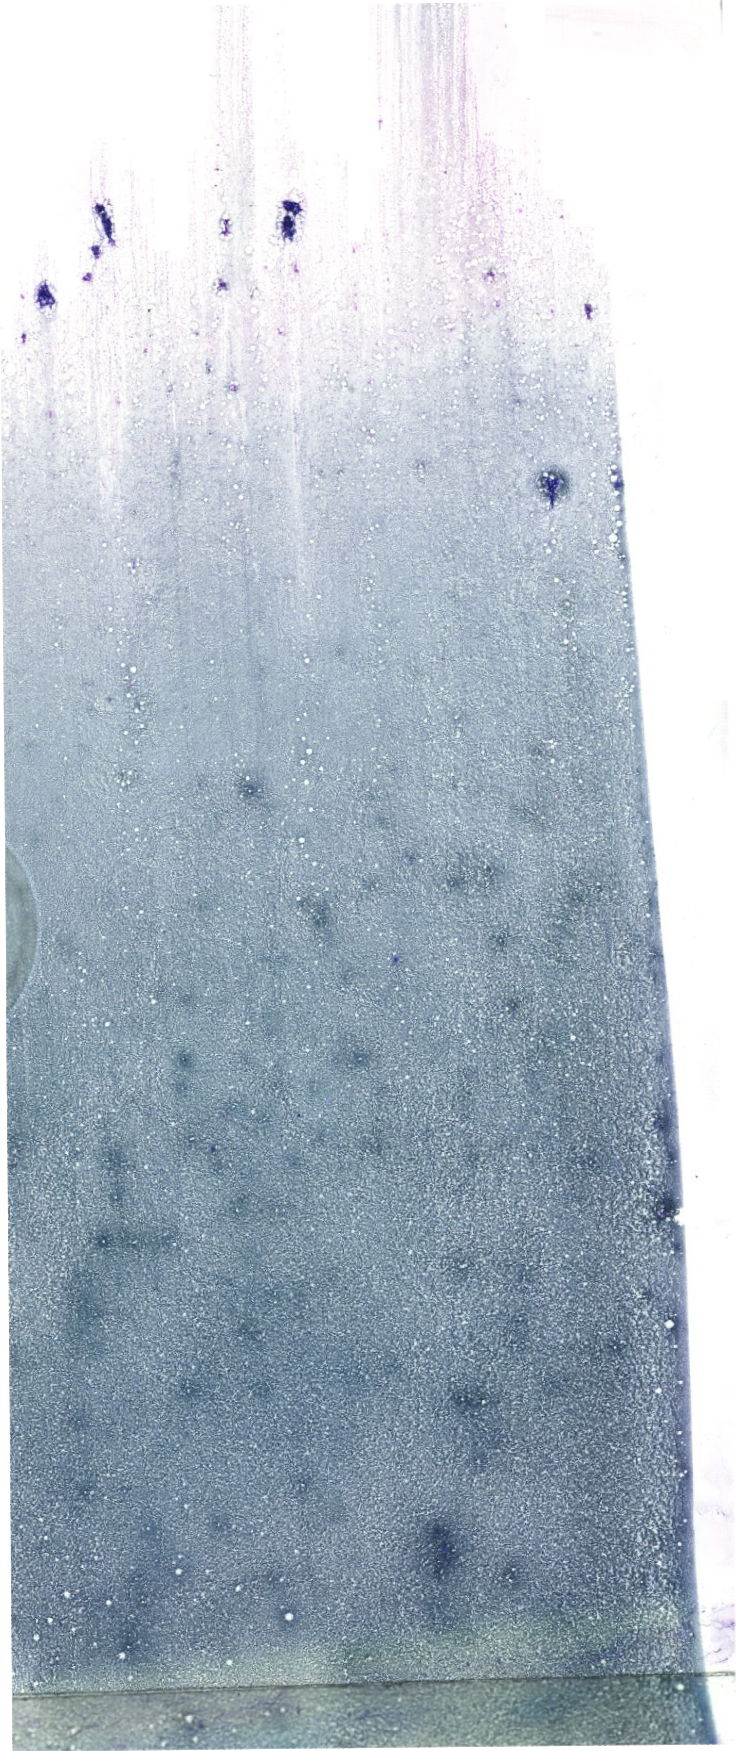
Bone marrow aspirate smear, May-Grünwald-Giemsa (MGG) stain, whole-slide image, low-resolution overview of the scanned area, about 20.9 x 49.6 mm. Female patient.
- diagnosis: Acute Myeloid Leukemia with Maturation